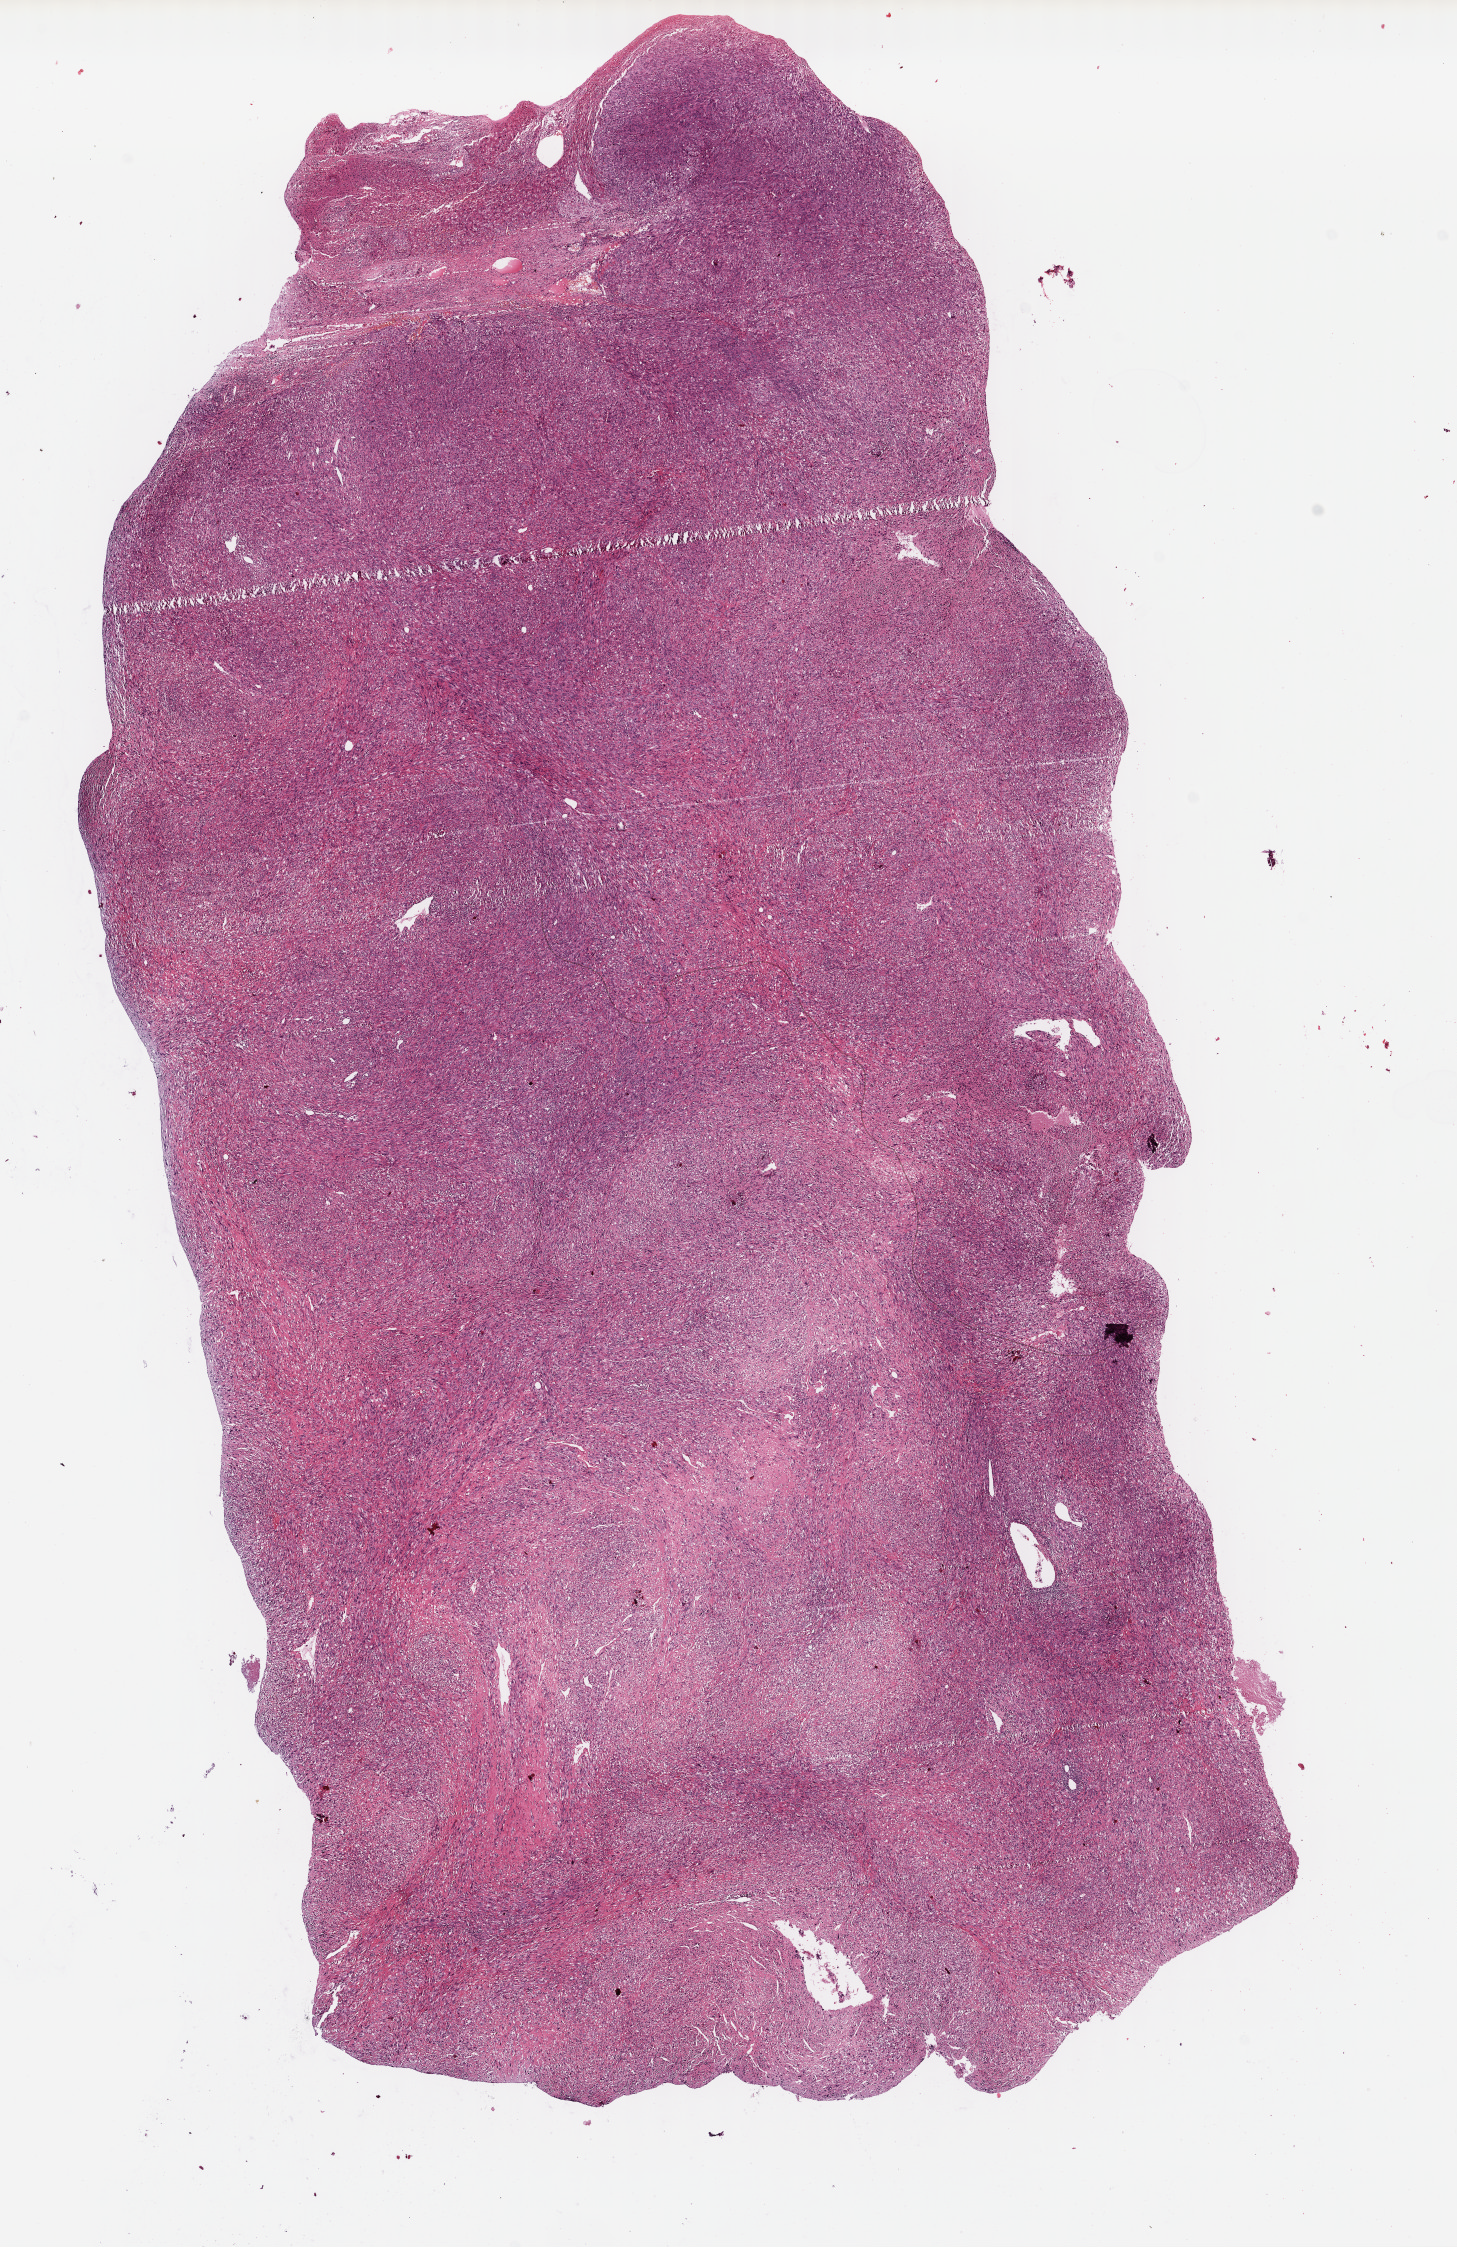
H&E whole-slide image — whole scanned area (about 11.5 x 17.7 mm) shown as a low-resolution overview, FFPE section, primary tumour sample from the liver. Male patient; age at initial diagnosis 45 years.
Pathologic diagnosis: Hepatocellular carcinoma, spindle cell variant.